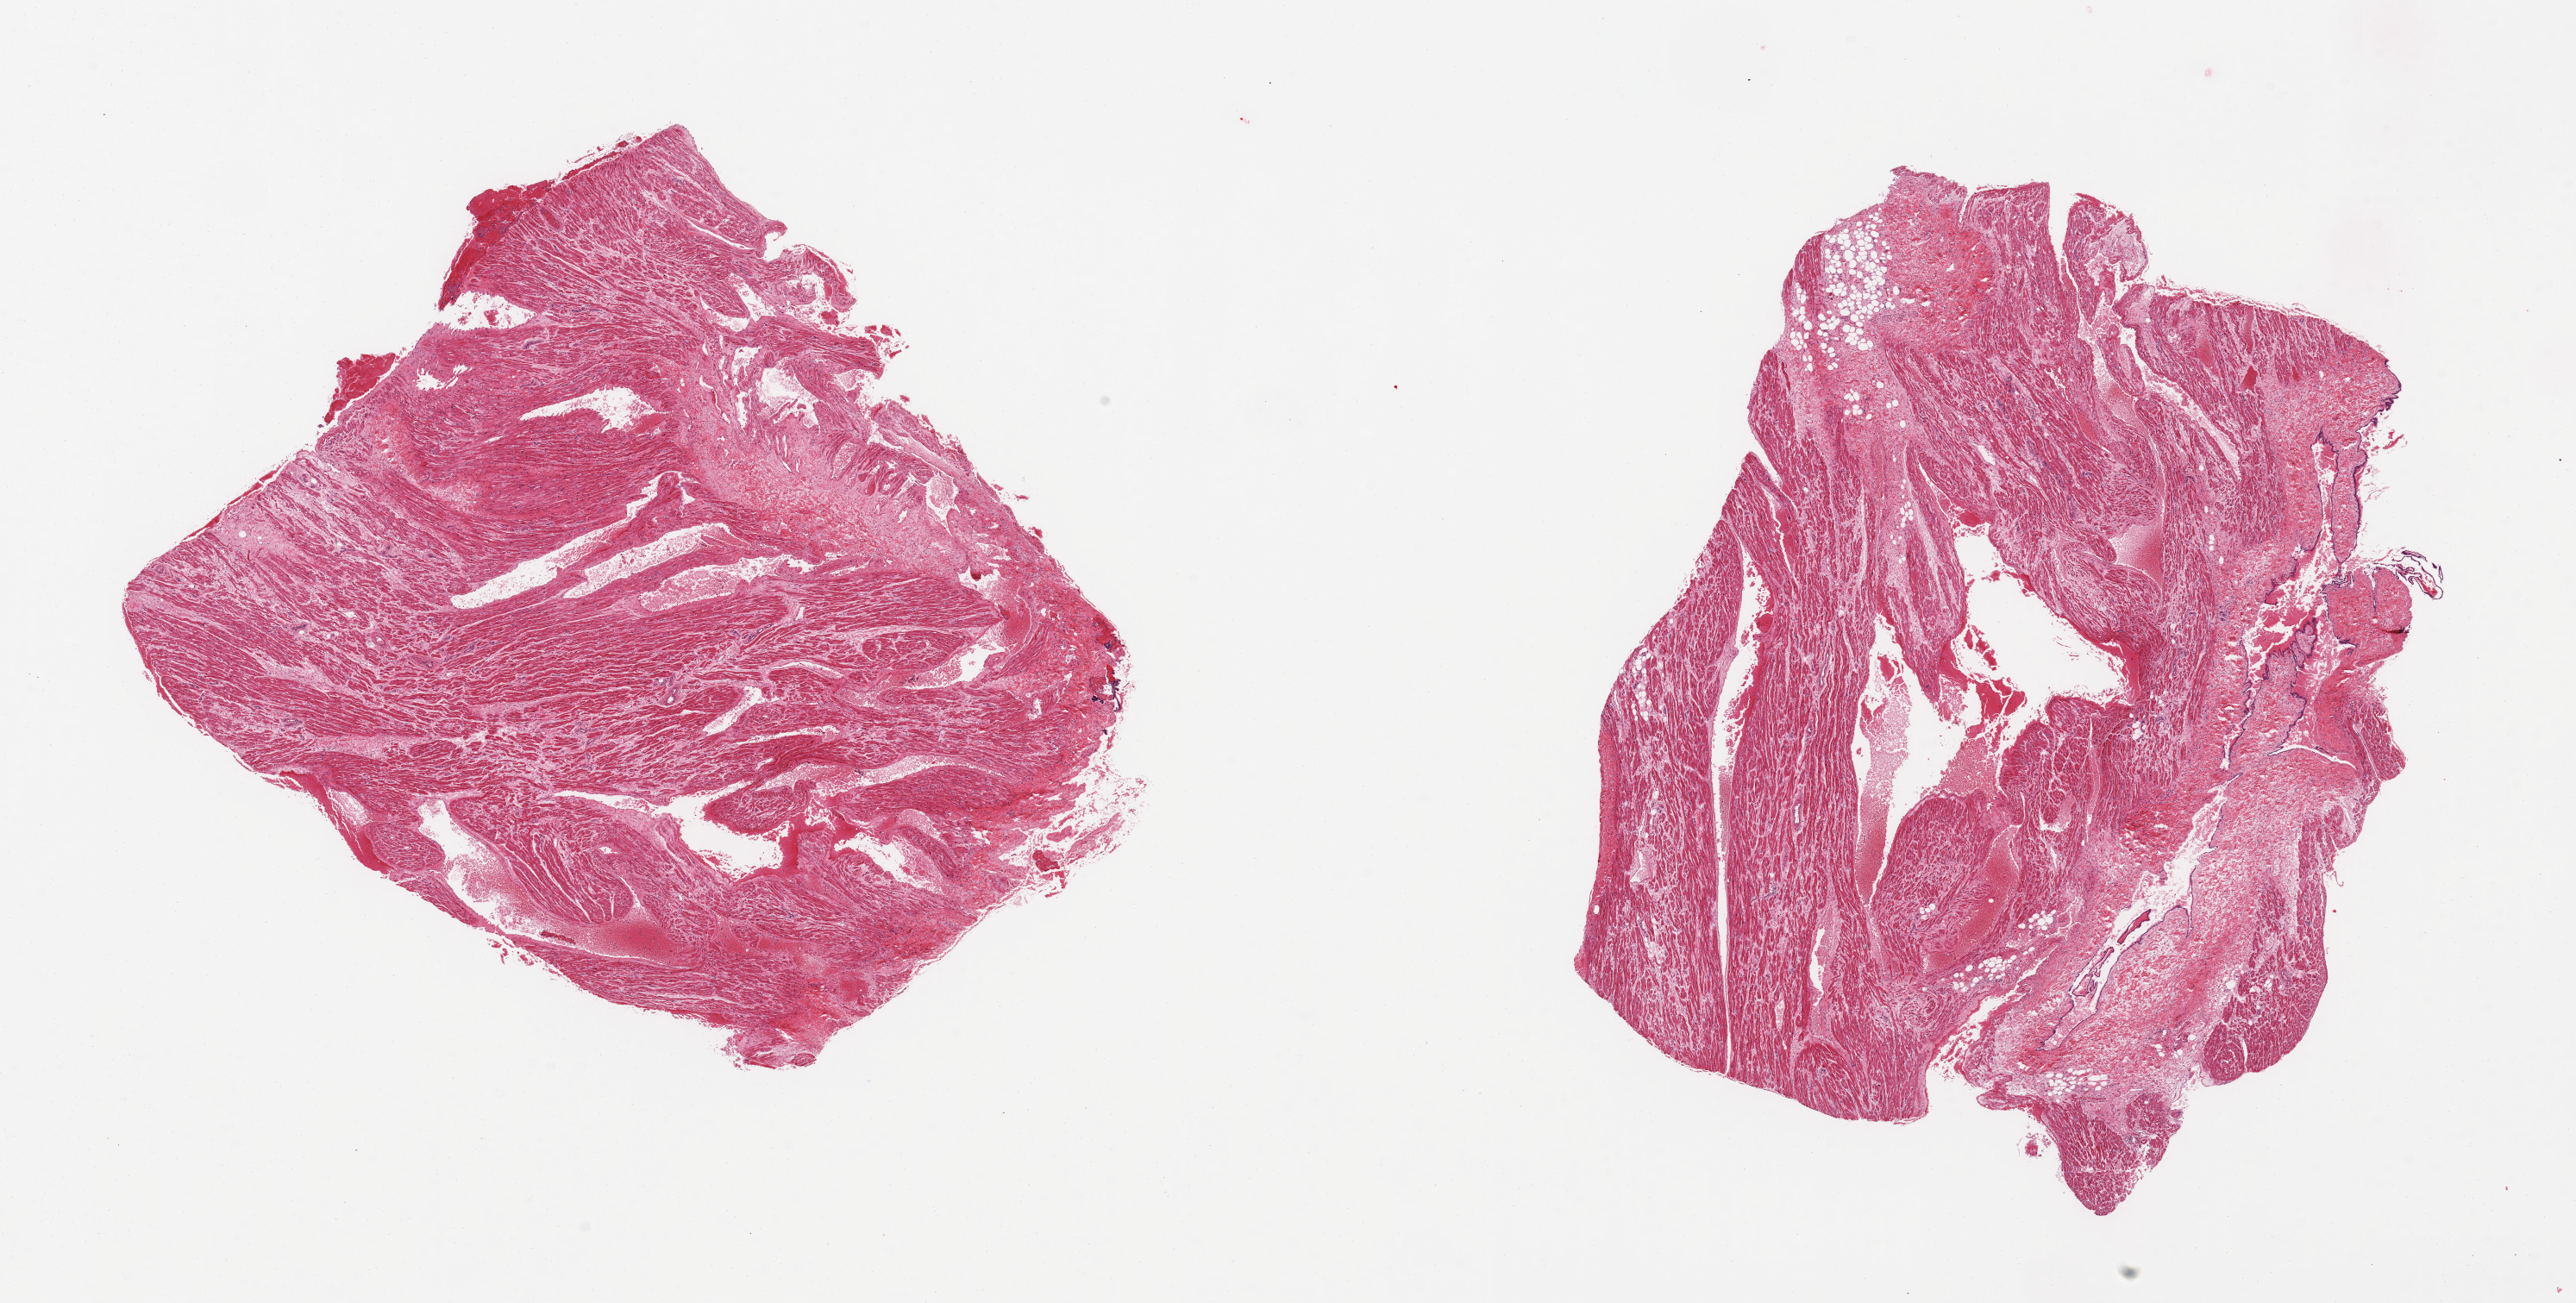
Whole-slide image, H&E stain — low-resolution overview of the scanned area, about 23.6 x 12.0 mm. PAXgene-fixed, paraffin-embedded tissue. Section of auricular appendage (target tissue). Tissue donor sample. Donor sex: male.
Pathologist's review note for this sample: 2 pieces, no abnormalities.